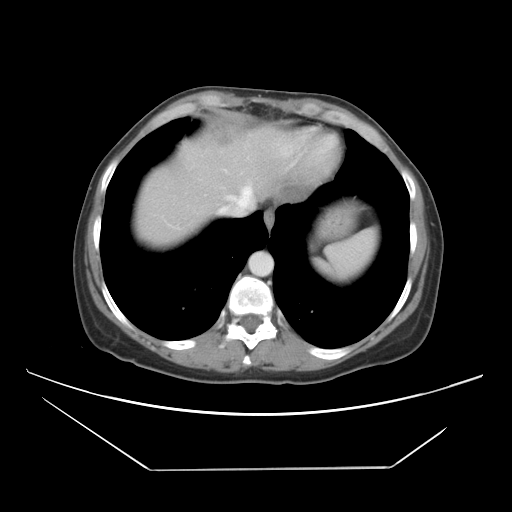
Contrast-enhanced abdominal CT, one axial slice. Position 37 of 42 along the scan axis. 120 kVp. Intravenous contrast given. Soft-tissue window (W 400 / L 40 HU). 5 mm slice thickness. 512 × 512 image matrix. Female patient, age 52 years. From the clinical record (not read from this slice): diagnosis: colorectal cancer liver metastases, imaged before liver resection; multiple liver metastases: yes; largest metastasis: 5.5 cm; disease in both lobes: yes.
Outlined on this slice (expert manual segmentation):
- hepatic veins: bounding box <221,186,253,214> (left, top, right, bottom; pixels)
- liver: <140,131,288,246>
- planned liver remnant (the part of the liver to remain after resection): <145,150,220,216>
- liver metastasis: <211,127,233,145>